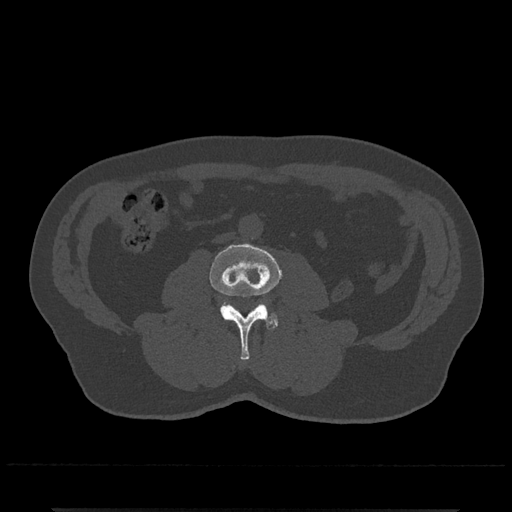
CT including the spine, one axial slice; position 210 of 797 along the scan axis; reconstruction kernel Br40s/3; bone window (W 1800 / L 400 HU); 0.5 mm slice thickness; 512 × 512 image matrix, field of view 393 × 393 mm. Male patient, age 67 years. Case-level facts recorded for this patient, not image findings: primary cancer: prostate.
Outlined on this slice (semi-automatic segmentation, software-assisted and operator-edited):
- L3 vertebra: bounding box [x1, y1, x2, y2] px = [209, 244, 282, 360]
- L4 vertebra: [222, 303, 279, 326]